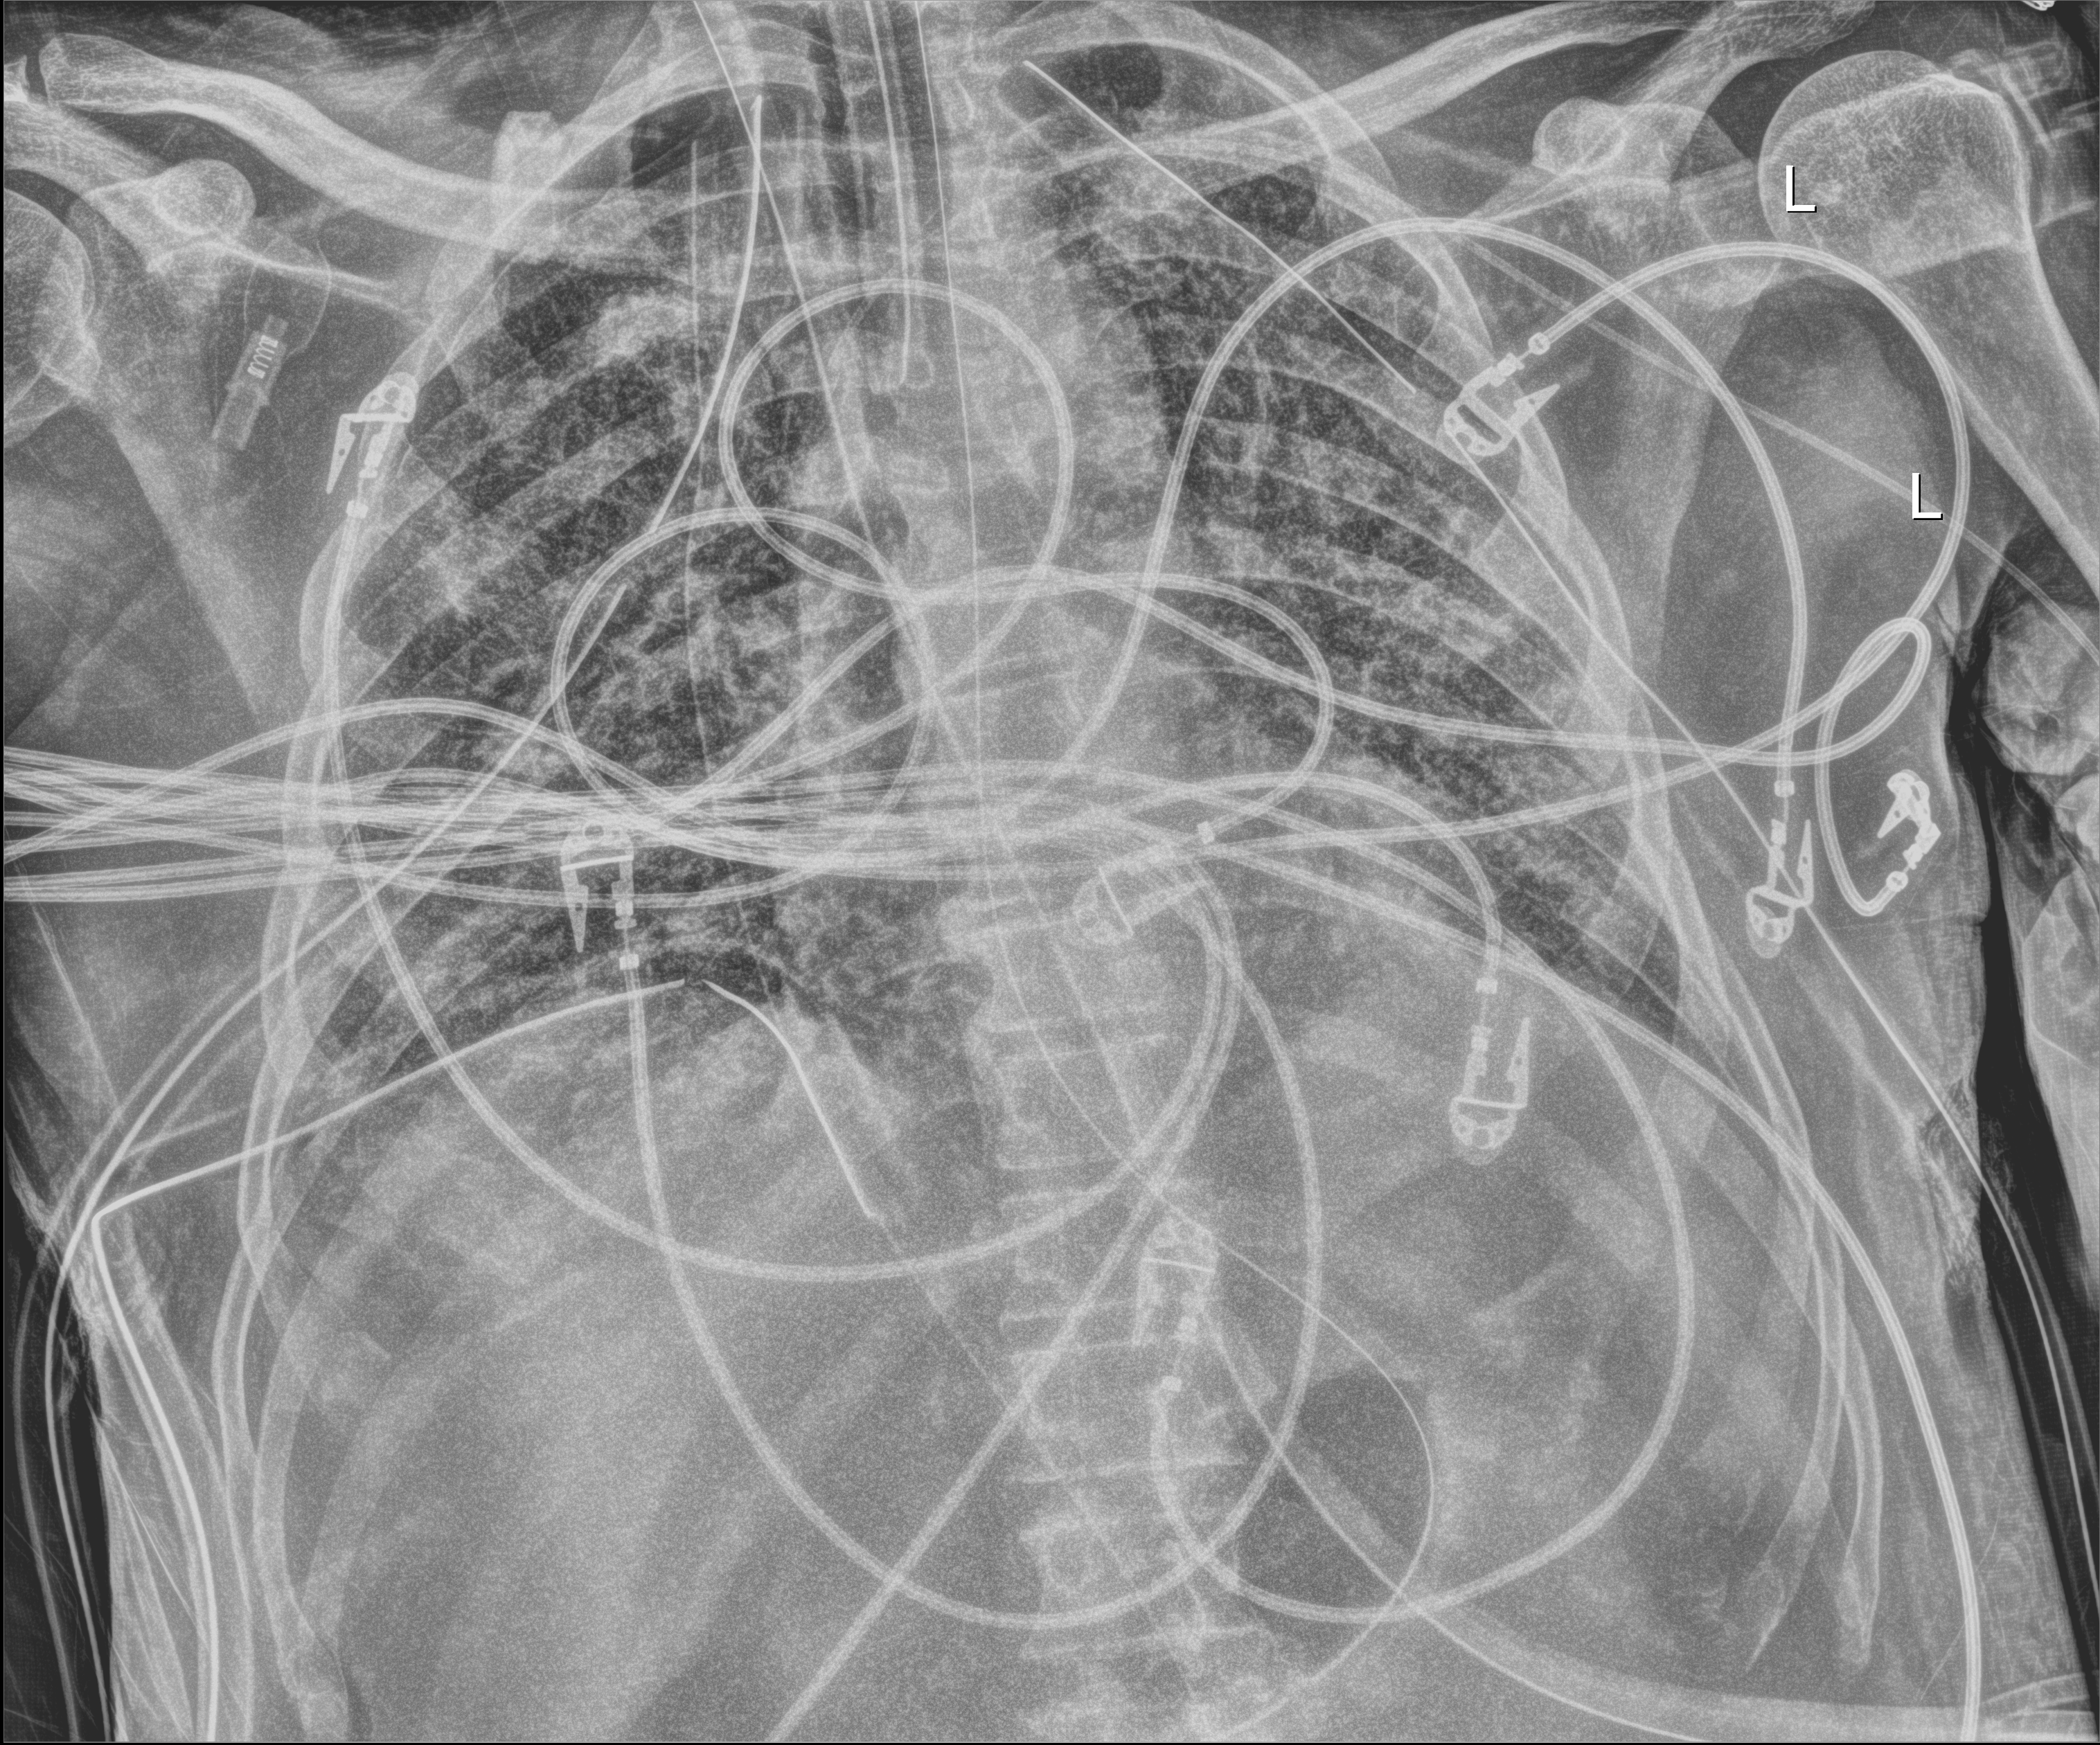
Bedside chest radiograph (digital radiography); anteroposterior (AP) projection. Male patient hospitalised with COVID-19, age 18–59 years.
From the hospital-stay record, not from the radiograph (when in the stay this image was taken is not recorded):
- length of hospital stay: 83 days
- other chronic lung disease (admission record): no
- smoking status (admission record): never